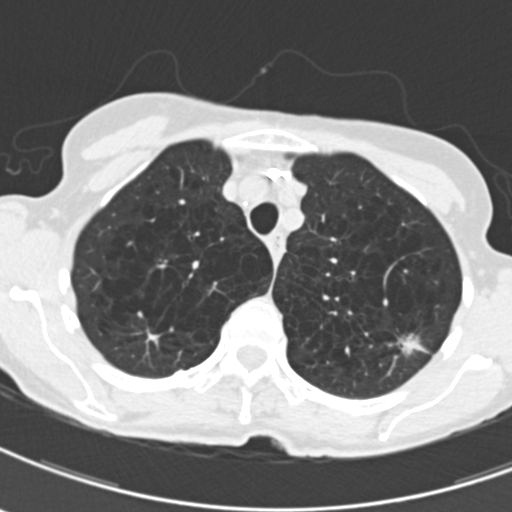
Chest CT (low-dose screening protocol), one axial image; third annual screen; lung window (W 1500 / L -600 HU); 2 mm slice thickness; standard (soft-tissue) reconstruction kernel (B30f); 120 kVp; slice 45 of 203 in the series. Female participant, aged 71 years at enrolment. Current smoker at enrolment.
• Lesion marked by an expert reader, bounding box (x1, y1, x2, y2) in pixels: (392, 323, 441, 367).
• Reader record for this screening exam (exam-level; its link to the box is not recorded): non-calcified nodule or mass ≥4 mm, left upper lobe, 12 × 9 mm, spiculated (stellate) margins, mixed attenuation, pre-existing on the prior screen: yes; interval growth: yes.
• Official screen result: positive, other.
• Later outcome: lung cancer diagnosed 114 days after this screen — adenocarcinoma, NOS, left upper lobe, moderately differentiated (G2), stage IA (AJCC 6th edition), 12 mm at pathology.